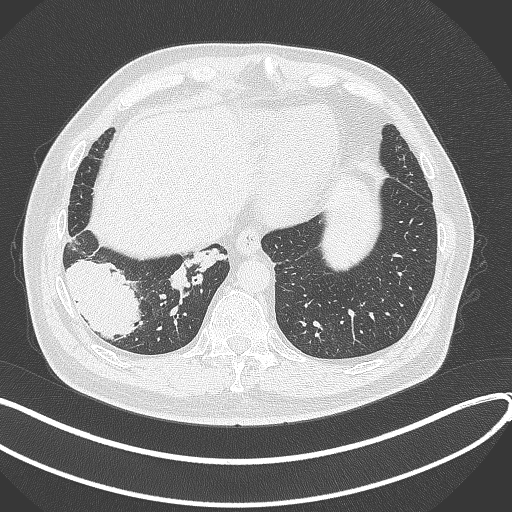
Chest CT, one axial slice; position 75 of 360 along the scan axis; lung window (W 1500 / L -600 HU); 1 mm slice thickness; 512 × 512 image matrix, field of view 400 × 400 mm. Patient: male, 59 years.
Outlined on this slice (bounding box drawn by a radiologist):
- lung tumour (recorded histology: adenocarcinoma): bounding box (x1, y1, x2, y2) in pixels: (65, 252, 150, 342)